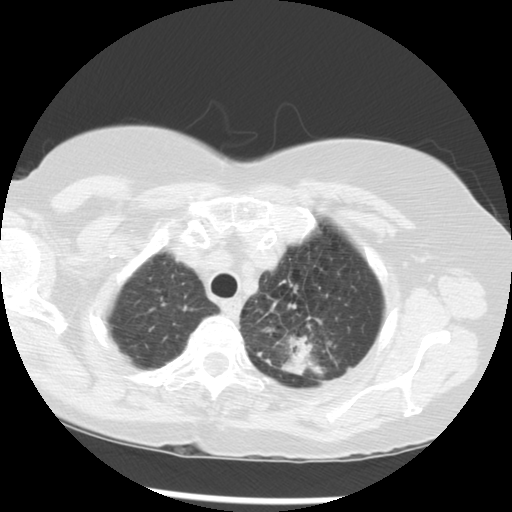
Low-dose screening chest CT, one axial slice. Slice 241 of 283 in the series (ordered by position). Reconstruction kernel STANDARD. Lung window (W 1500 / L -600 HU). 2.5 mm slice thickness. 512 × 512 image matrix, field of view 330 × 330 mm.
Annotated regions visible in this slice (expert manual segmentation):
- lesion 1 (tumor, upper lobe of left lung): bounding box <282,335,314,375> (left, top, right, bottom; pixels)